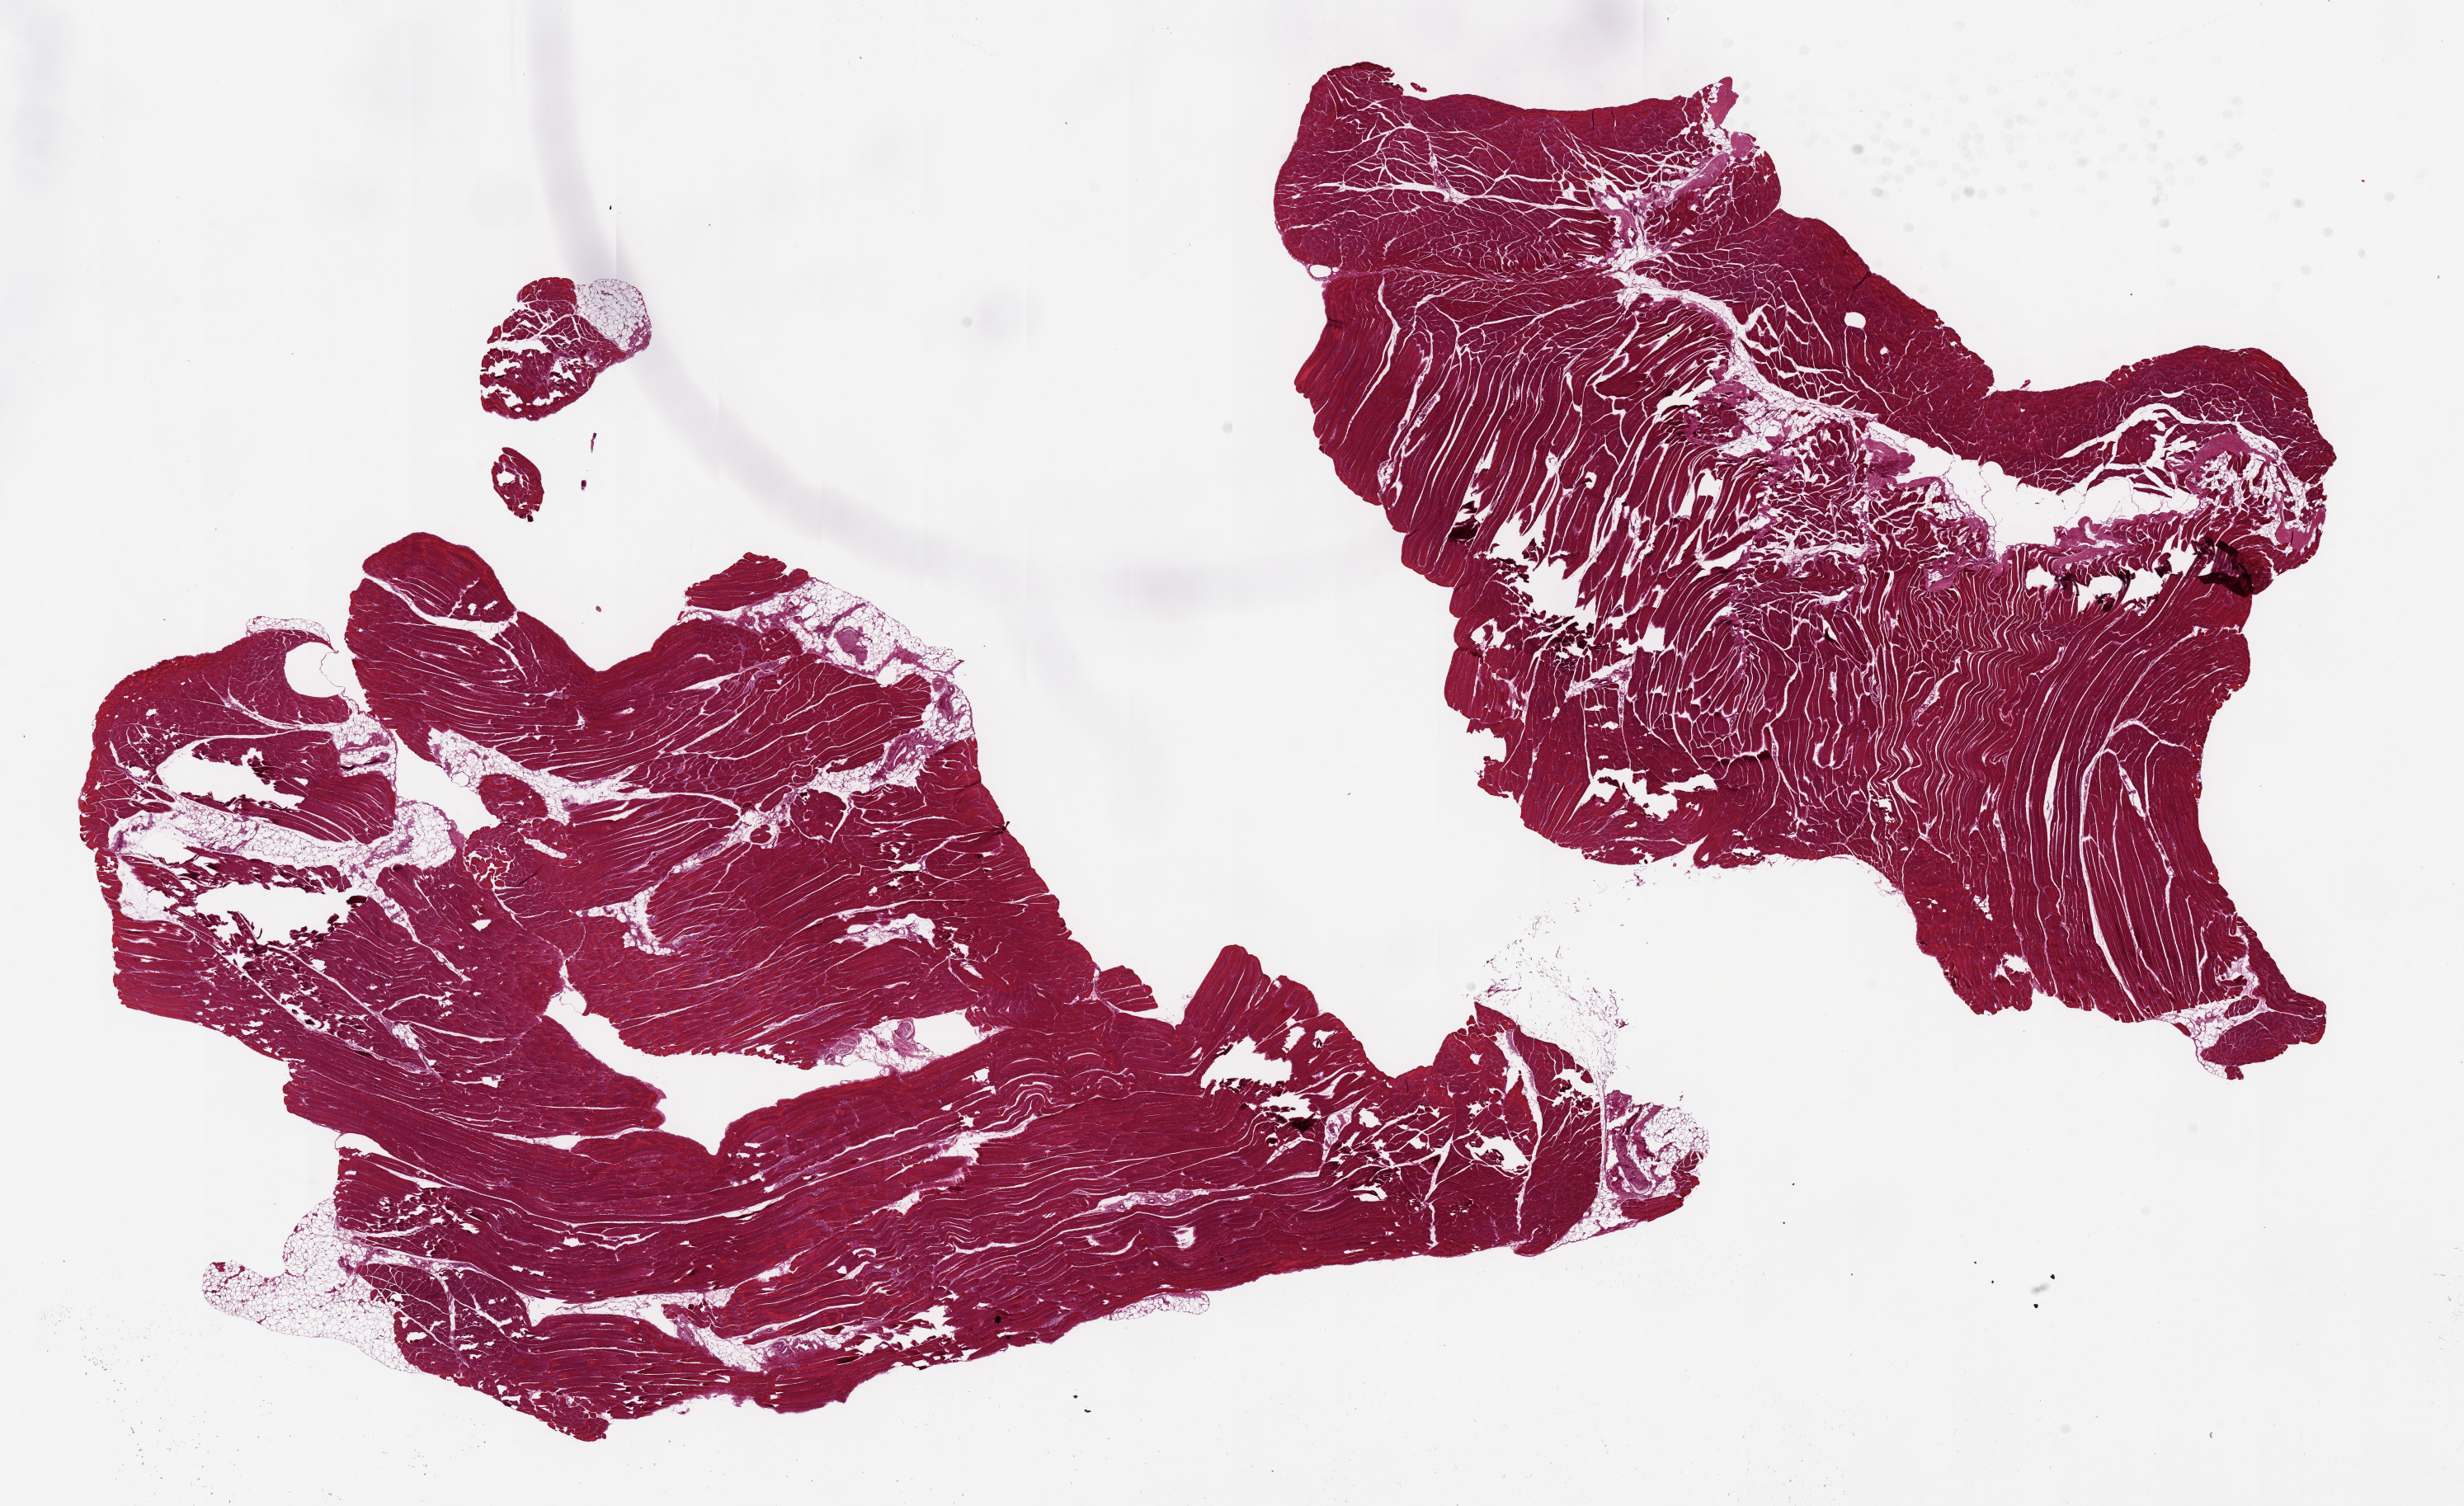
H&E whole-slide image, low-resolution overview of the scanned area, about 23.6 x 14.4 mm (acquisition: 20x scan), PAXgene-fixed, paraffin-embedded tissue, sampled site (target tissue): skeletal muscle, donor tissue sample. Donor: male.
- pathologist's review note for this sample: 2 pieces 11x9 & 9x7 mm; <10% adipose